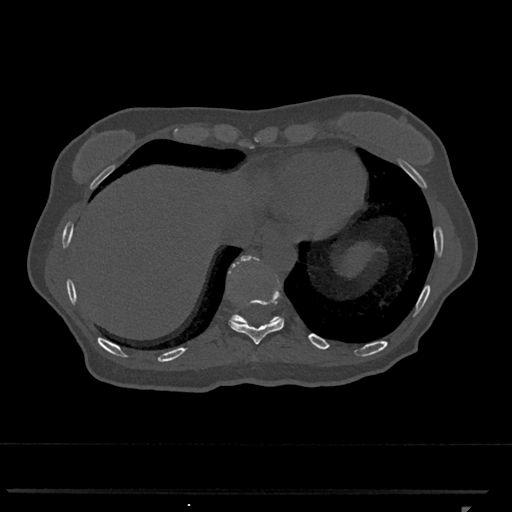
CT including the spine, one axial slice; position 558 of 793 along the scan axis; reconstruction kernel Br40s/3; bone window (W 1800 / L 400 HU); 0.5 mm slice thickness; 512 × 512 image matrix, field of view 380 × 380 mm. Patient: female, 62 years. From the clinical record (not read from this slice): primary cancer: renal.
Annotated regions visible in this slice (semi-automatic segmentation, software-assisted and operator-edited):
- T10 vertebra: bounding box [x1, y1, x2, y2] px = [229, 268, 284, 345]
- T11 vertebra: [228, 255, 281, 324]